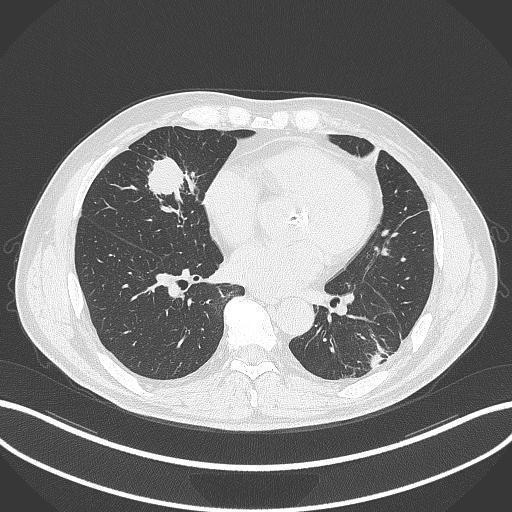
Chest CT, one axial slice. Slice 118 of 399 in the series (ordered by position). Reconstruction kernel B70f. 120 kVp. Lung window (W 1500 / L -600 HU). 512 × 512 image matrix. Male patient, age 59 years. From the clinical record (not read from this slice): clinical TNM (as recorded): T2a N1 M0.
Annotated regions visible in this slice (bounding box drawn by a radiologist):
- lung tumour (recorded histology: adenocarcinoma): bounding box <140,150,192,213> (left, top, right, bottom; pixels)